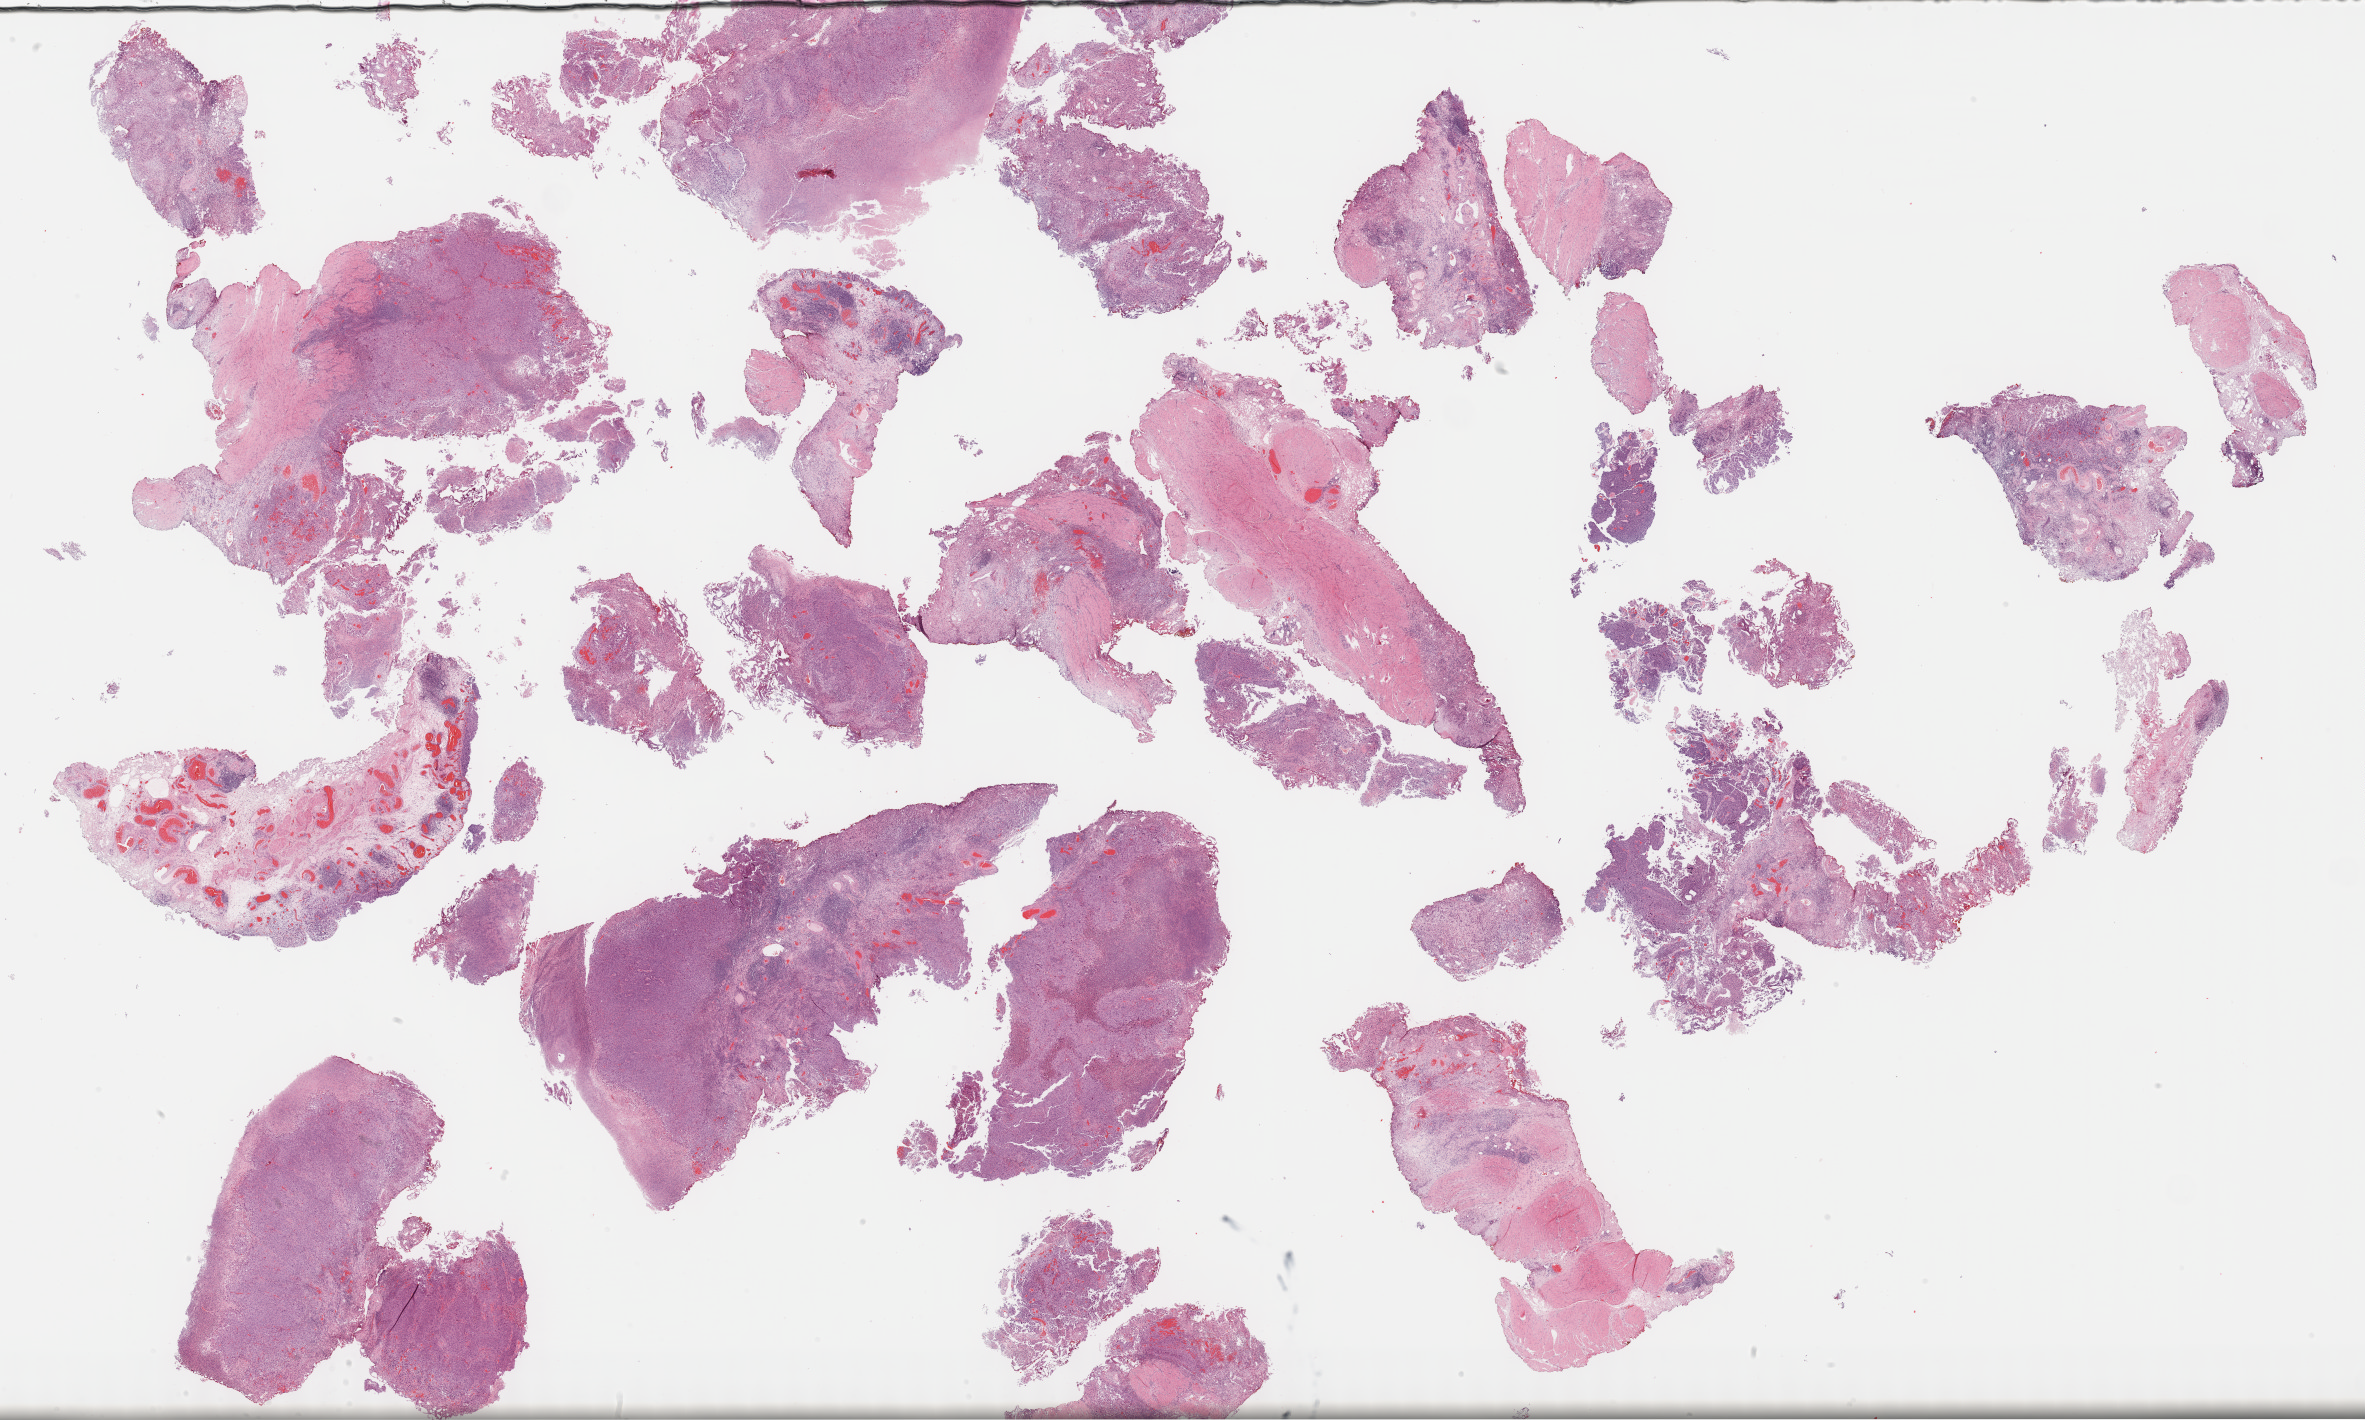
Whole-slide histology image, H&E, a low-resolution overview of the entire scanned area, about 38.3 x 23.0 mm, formalin-fixed paraffin-embedded (FFPE) diagnostic section, primary tumour sample from the bladder. Male patient; age at initial diagnosis 56 years. Histologic grade: high grade.
Histologic diagnosis: Transitional cell carcinoma. AJCC pathologic stage: II.